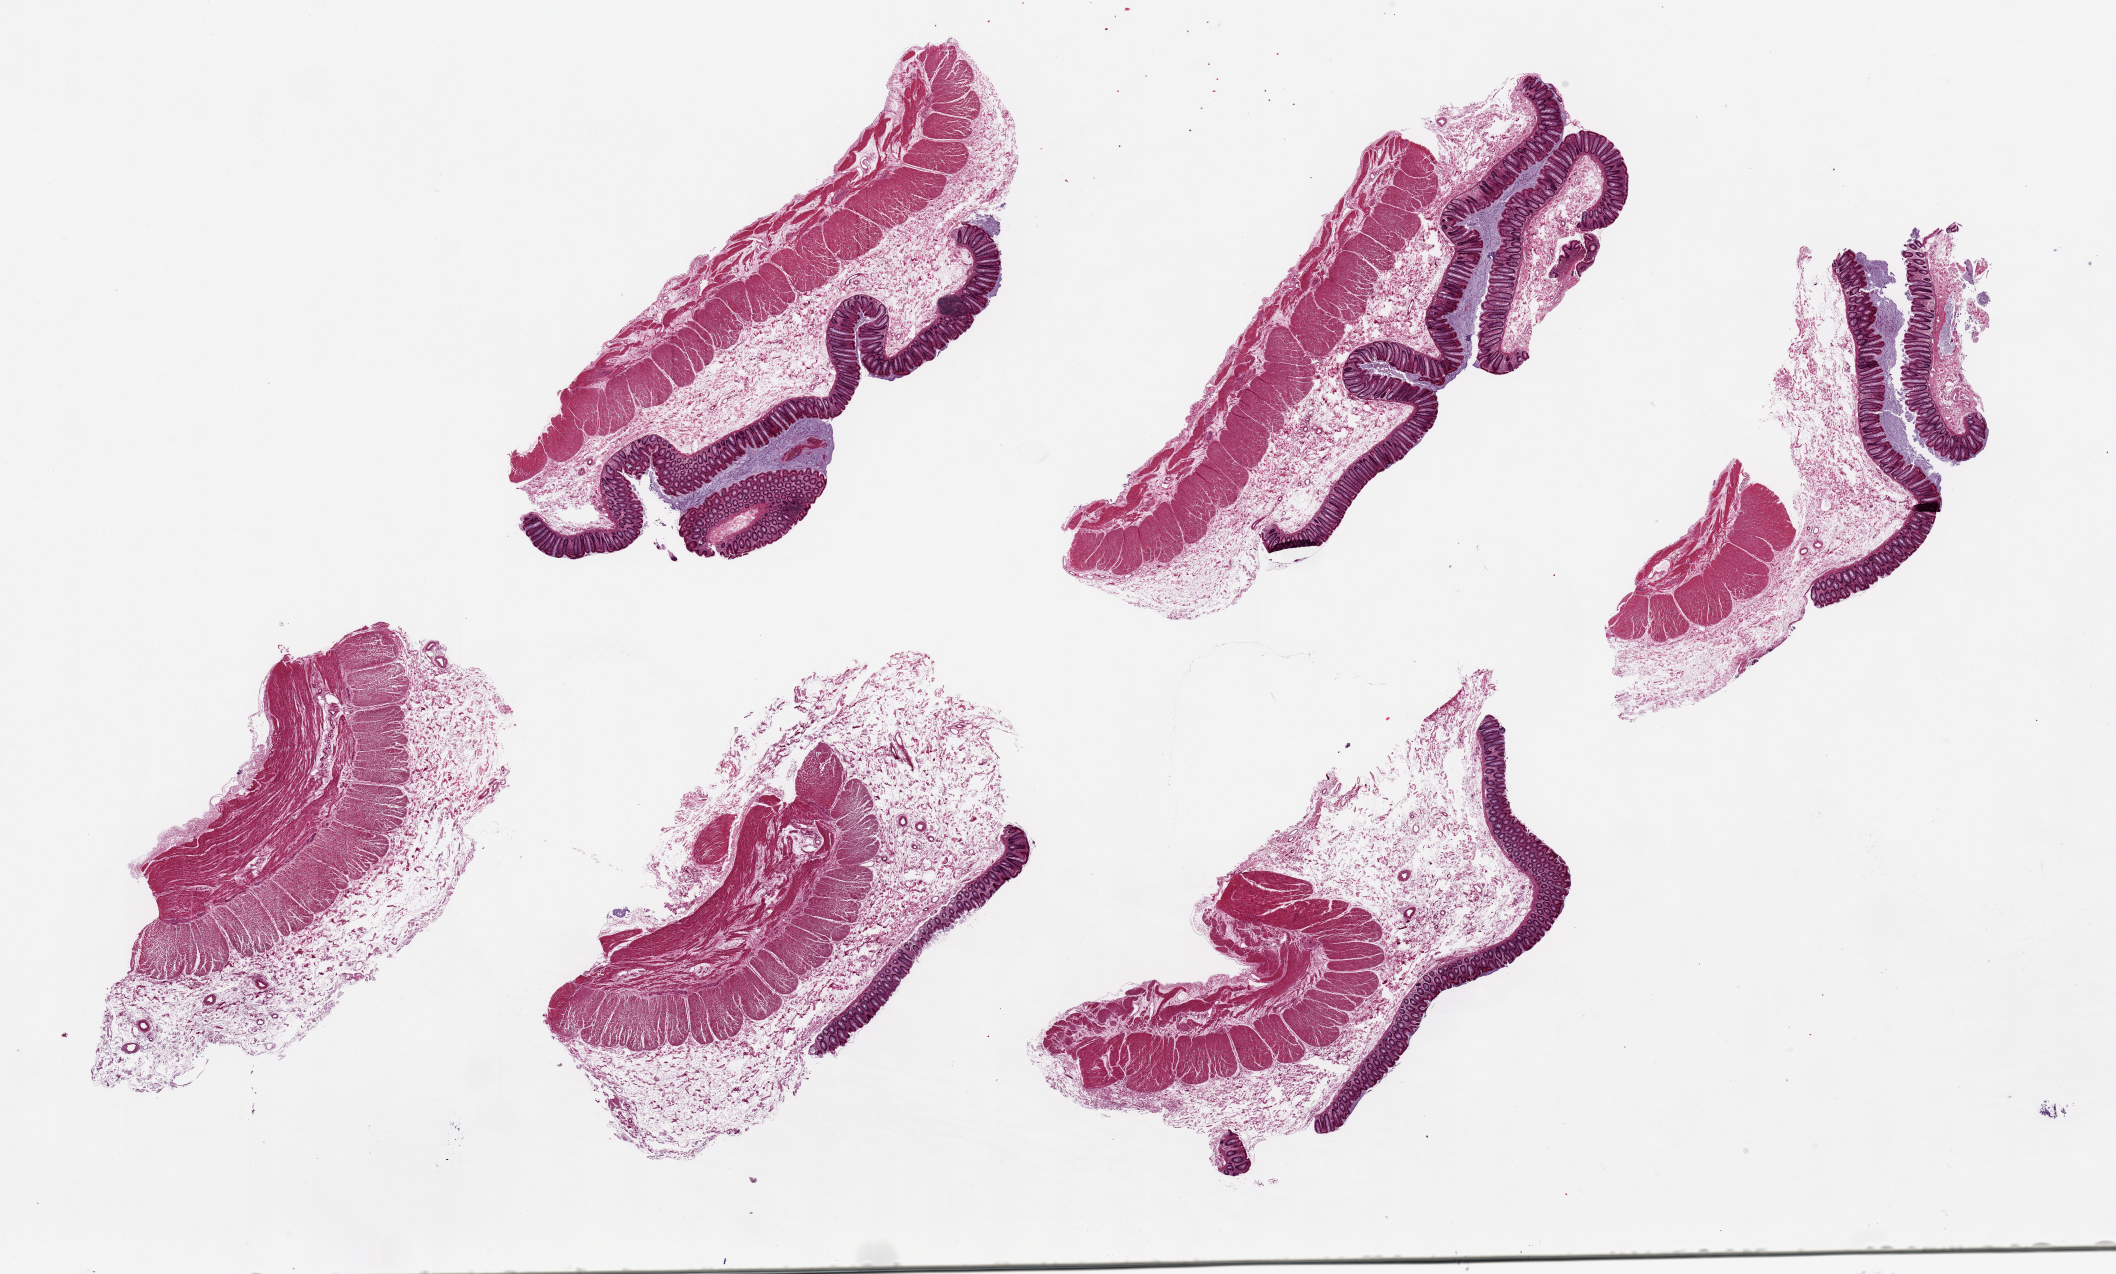
Digitized haematoxylin and eosin-stained section — a low-resolution overview of the entire scanned area, about 33.5 x 20.2 mm, PAXgene-fixed, paraffin-embedded tissue, target tissue: transverse colon, tissue donor sample. Donor: female.
Reviewer comment on this tissue sample: 6 pieces, ~9x3mm. Mucosa well preserved, ~10-15% of thickness.